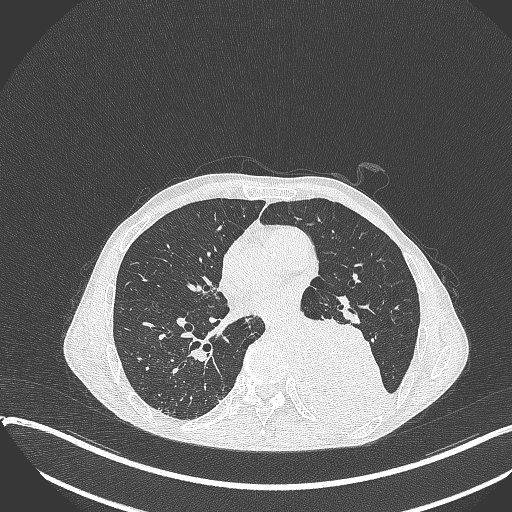
Chest CT, one axial slice; slice 170 of 401 in the series (ordered by position); reconstruction kernel B70f; lung window (W 1500 / L -600 HU); 1 mm slice thickness; 512 × 512 image matrix, field of view 400 × 400 mm. Male patient, age 57 years. Case-level facts recorded for this patient, not image findings: clinical TNM (as recorded): T4 N0 M0.
Structures marked on this image (bounding box drawn by a radiologist):
- lung tumour (recorded histology: squamous cell carcinoma): bounding box (x1, y1, x2, y2) in pixels: (294, 308, 394, 428)